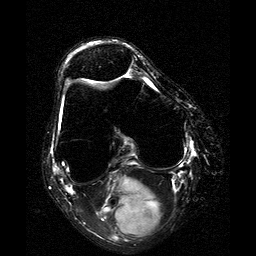
MRI of an extremity soft-tissue mass, one axial slice; slice 8 of 25 in the series (ordered by position); T2-weighted fat-saturated; 256 × 256 image matrix. Female patient. Case-level facts recorded for this patient, not image findings: histological type: liposarcoma; site of the primary tumour: right thigh.
Annotated regions visible in this slice (expert manual segmentation):
- gross tumour volume (mass): box from (x=96, y=174) to (x=161, y=238) px